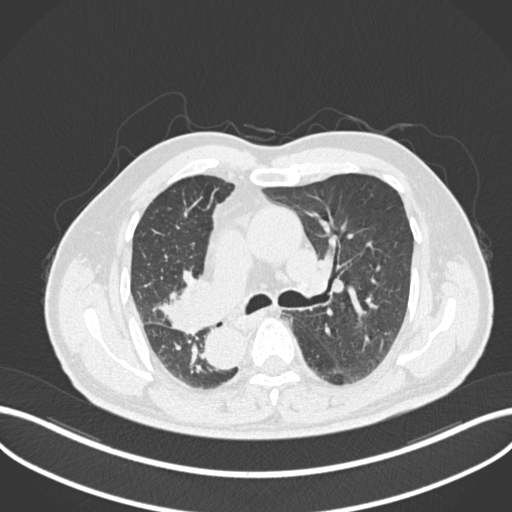
Chest CT, one axial slice; slice 142 of 206 in the series (ordered by position); 120 kVp; lung window (W 1500 / L -600 HU); 512 × 512 image matrix, field of view 400 × 400 mm. Male patient, age 67 years. From the clinical record (not read from this slice): clinical TNM (as recorded): T2a N0 M0.
Structures marked on this image (bounding box drawn by a radiologist):
- lung tumour (recorded histology: squamous cell carcinoma): bounding box <154,268,217,334> (left, top, right, bottom; pixels)